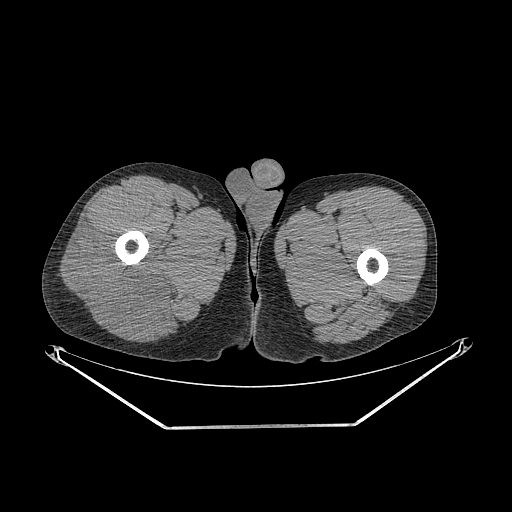
CT of an extremity soft-tissue mass (from a PET/CT study), one axial slice. Slice 265 of 267 in the series (ordered by position). 140 kVp. Soft-tissue window (W 400 / L 40 HU). 512 × 512 image matrix, field of view 500 × 500 mm. Male patient. From the clinical record (not read from this slice): histological type: poorly differentiated synovial sarcoma; grade: high; site of the primary tumour: right buttock.
Structures marked on this image (expert contour drawn on MRI and transferred to this co-registered scan by the dataset authors):
- gross tumour volume including surrounding oedema: box from (x=60, y=226) to (x=177, y=334) px
- gross tumour volume (mass): (x=60, y=226)–(x=165, y=334)